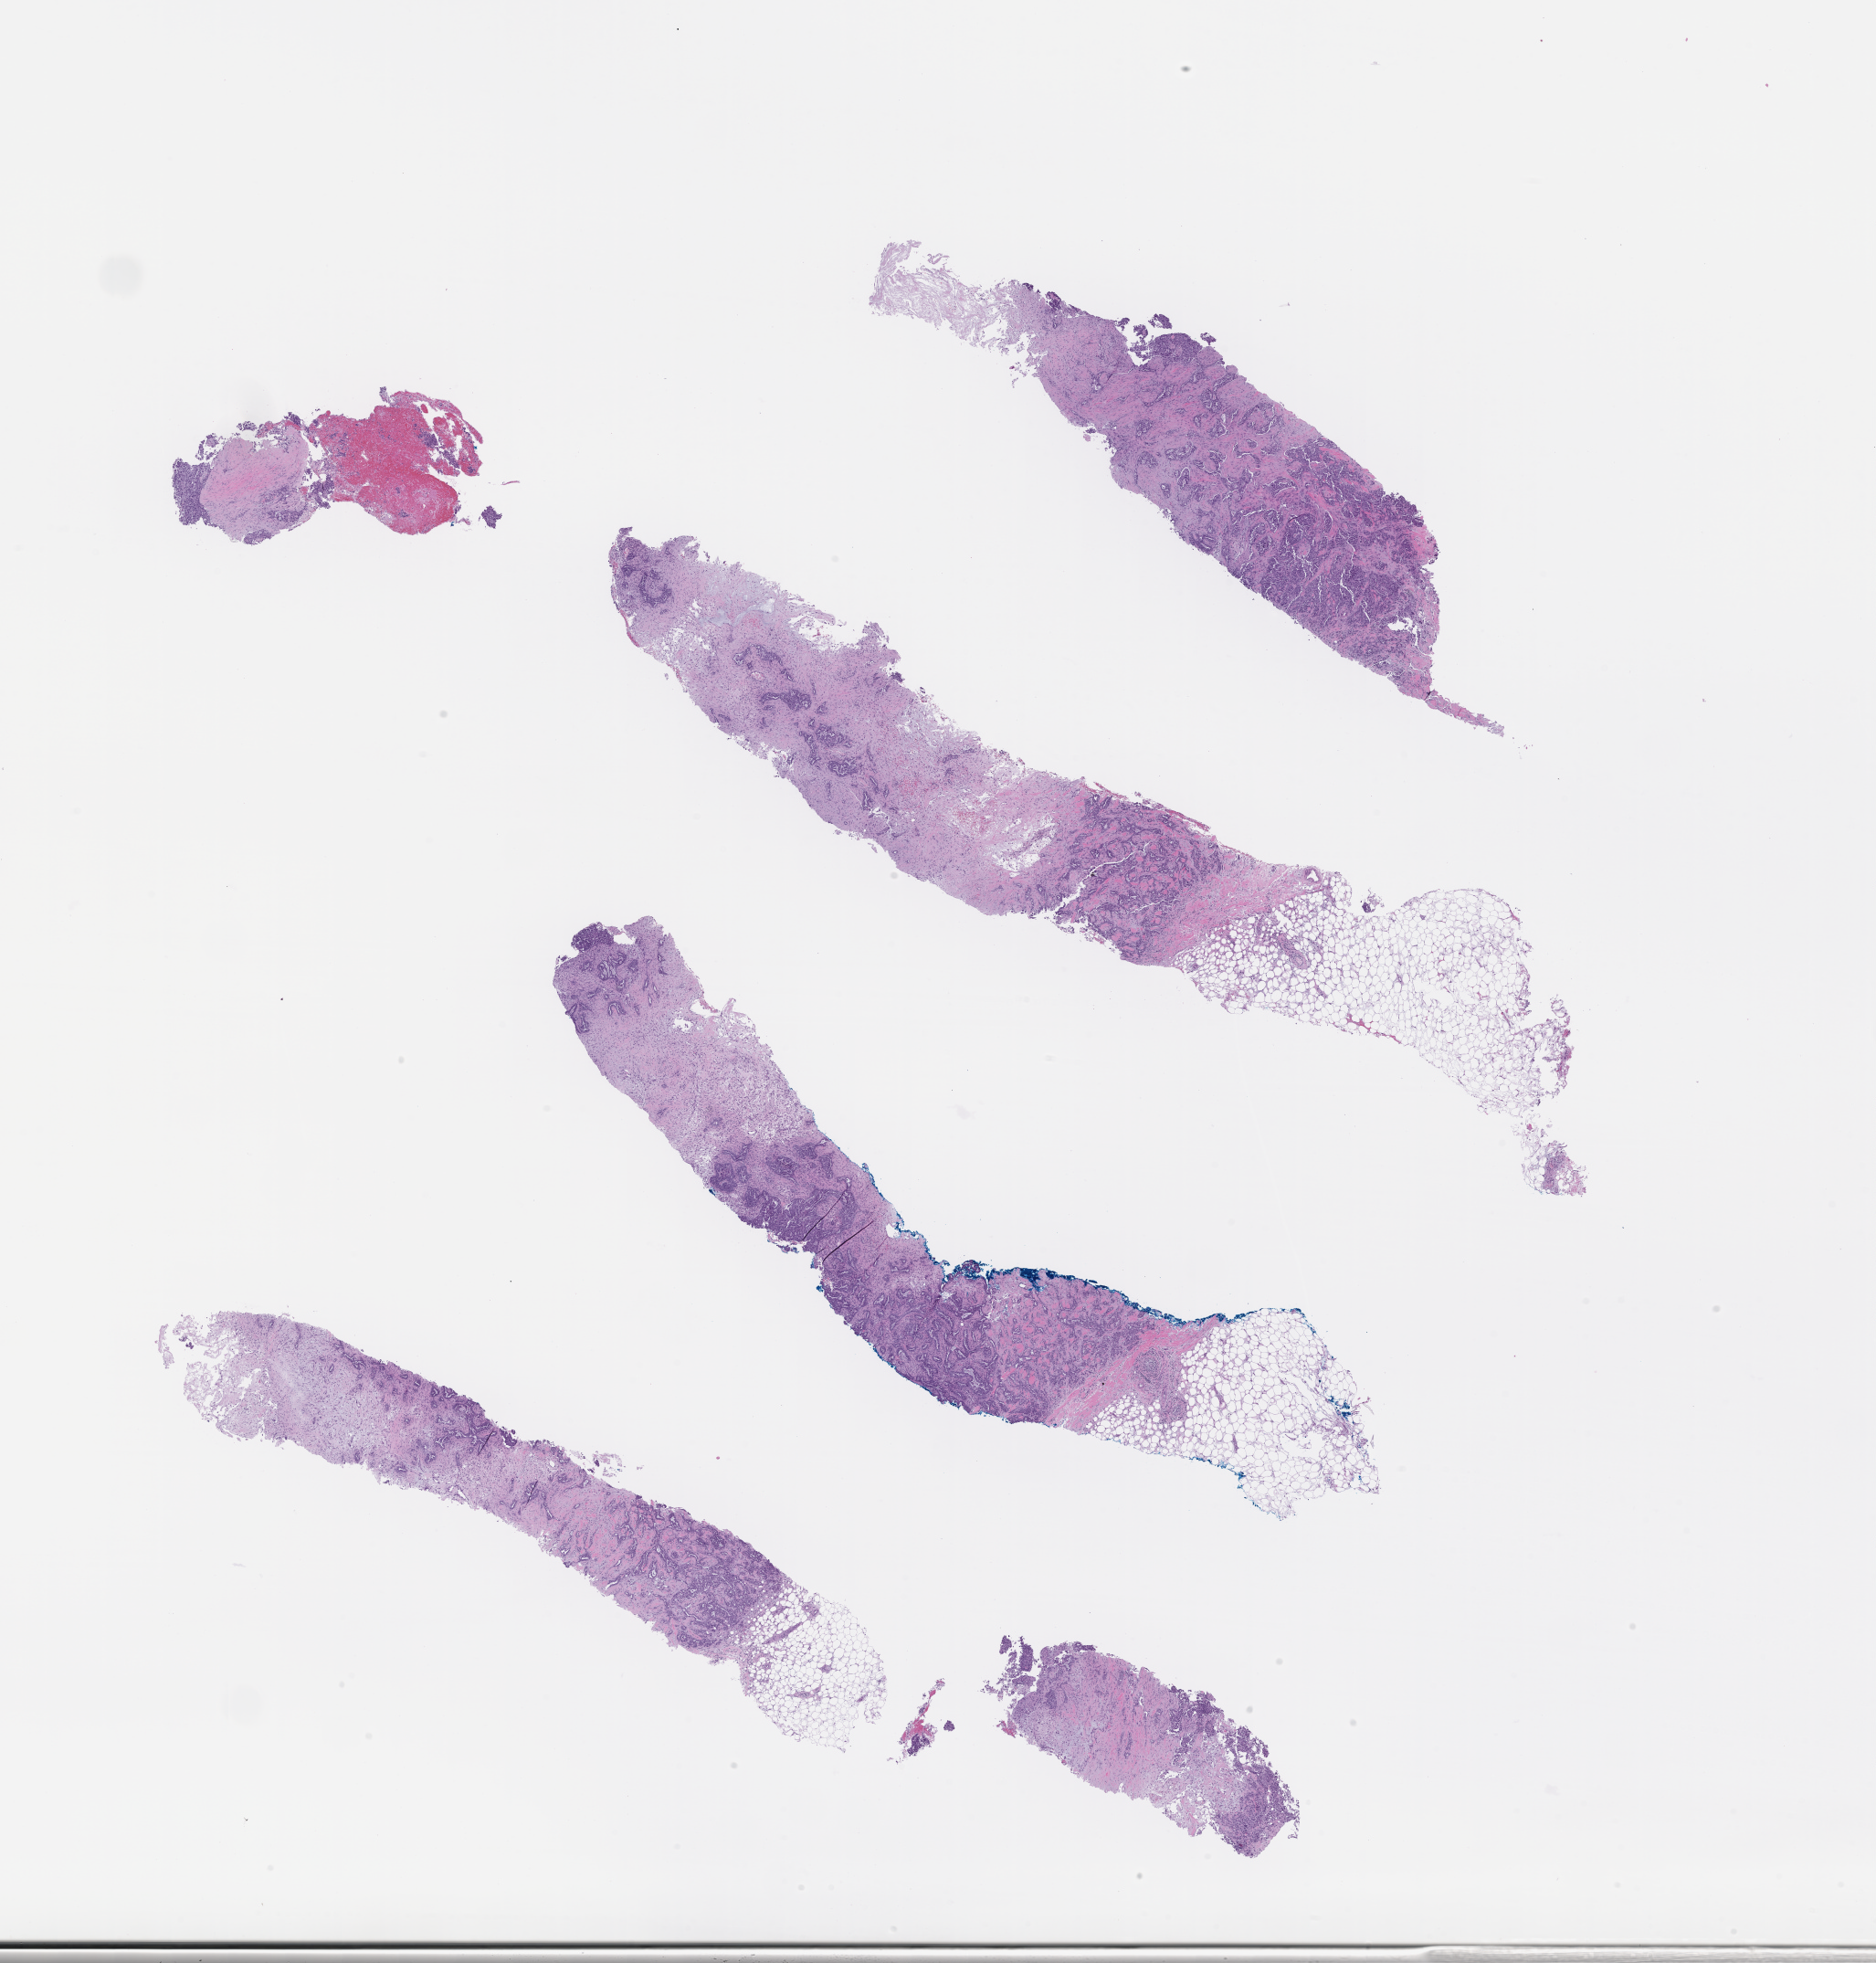
Digitized H&E-stained section, whole scanned area (about 16.6 x 17.4 mm) shown as a low-resolution overview. Formalin-fixed, paraffin-embedded (FFPE) tissue. Tissue site: breast. Archival tissue. Female patient.
This section: primary tumour tissue. Diagnosis: Invasive Breast Carcinoma.